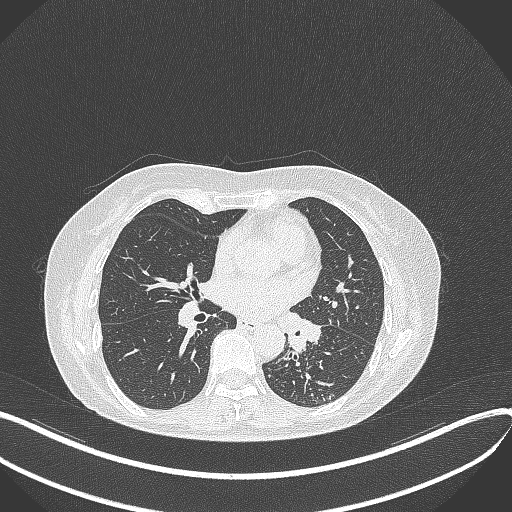
Chest CT, one axial slice; slice 203 of 429 in the series (ordered by position); reconstruction kernel B70f; 100 kVp; lung window (W 1500 / L -600 HU); 1 mm slice thickness; 512 × 512 image matrix. Patient: female, 63 years. Case-level facts recorded for this patient, not image findings: clinical TNM (as recorded): T1b N0 M0; histopathological grade: G2-3.
Outlined on this slice (rectangle marked by the reading radiologist):
- lung tumour (recorded histology: adenocarcinoma): bounding box (x1, y1, x2, y2) in pixels: (278, 311, 321, 355)